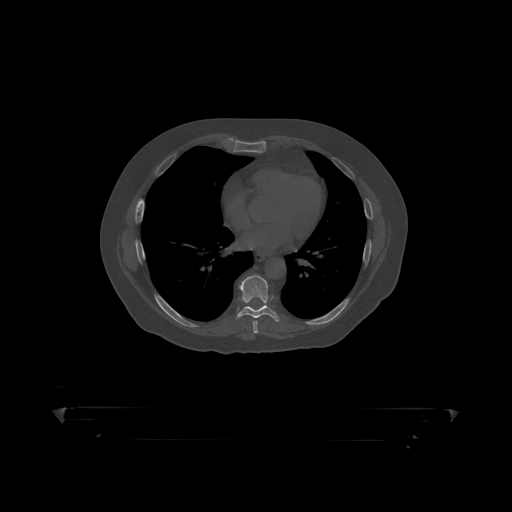
CT including the spine, one axial slice; slice 259 of 390 in the series (ordered by position); reconstruction kernel STANDARD; 120 kVp; bone window (W 1800 / L 400 HU); 1.25 mm slice thickness; 512 × 512 image matrix. Male patient, age 60 years. Case-level facts recorded for this patient, not image findings: primary cancer: prostate.
Annotated regions visible in this slice (semi-automatic segmentation, software-assisted and operator-edited):
- T8 vertebra: bounding box (x1, y1, x2, y2) in pixels: (237, 275, 277, 319)